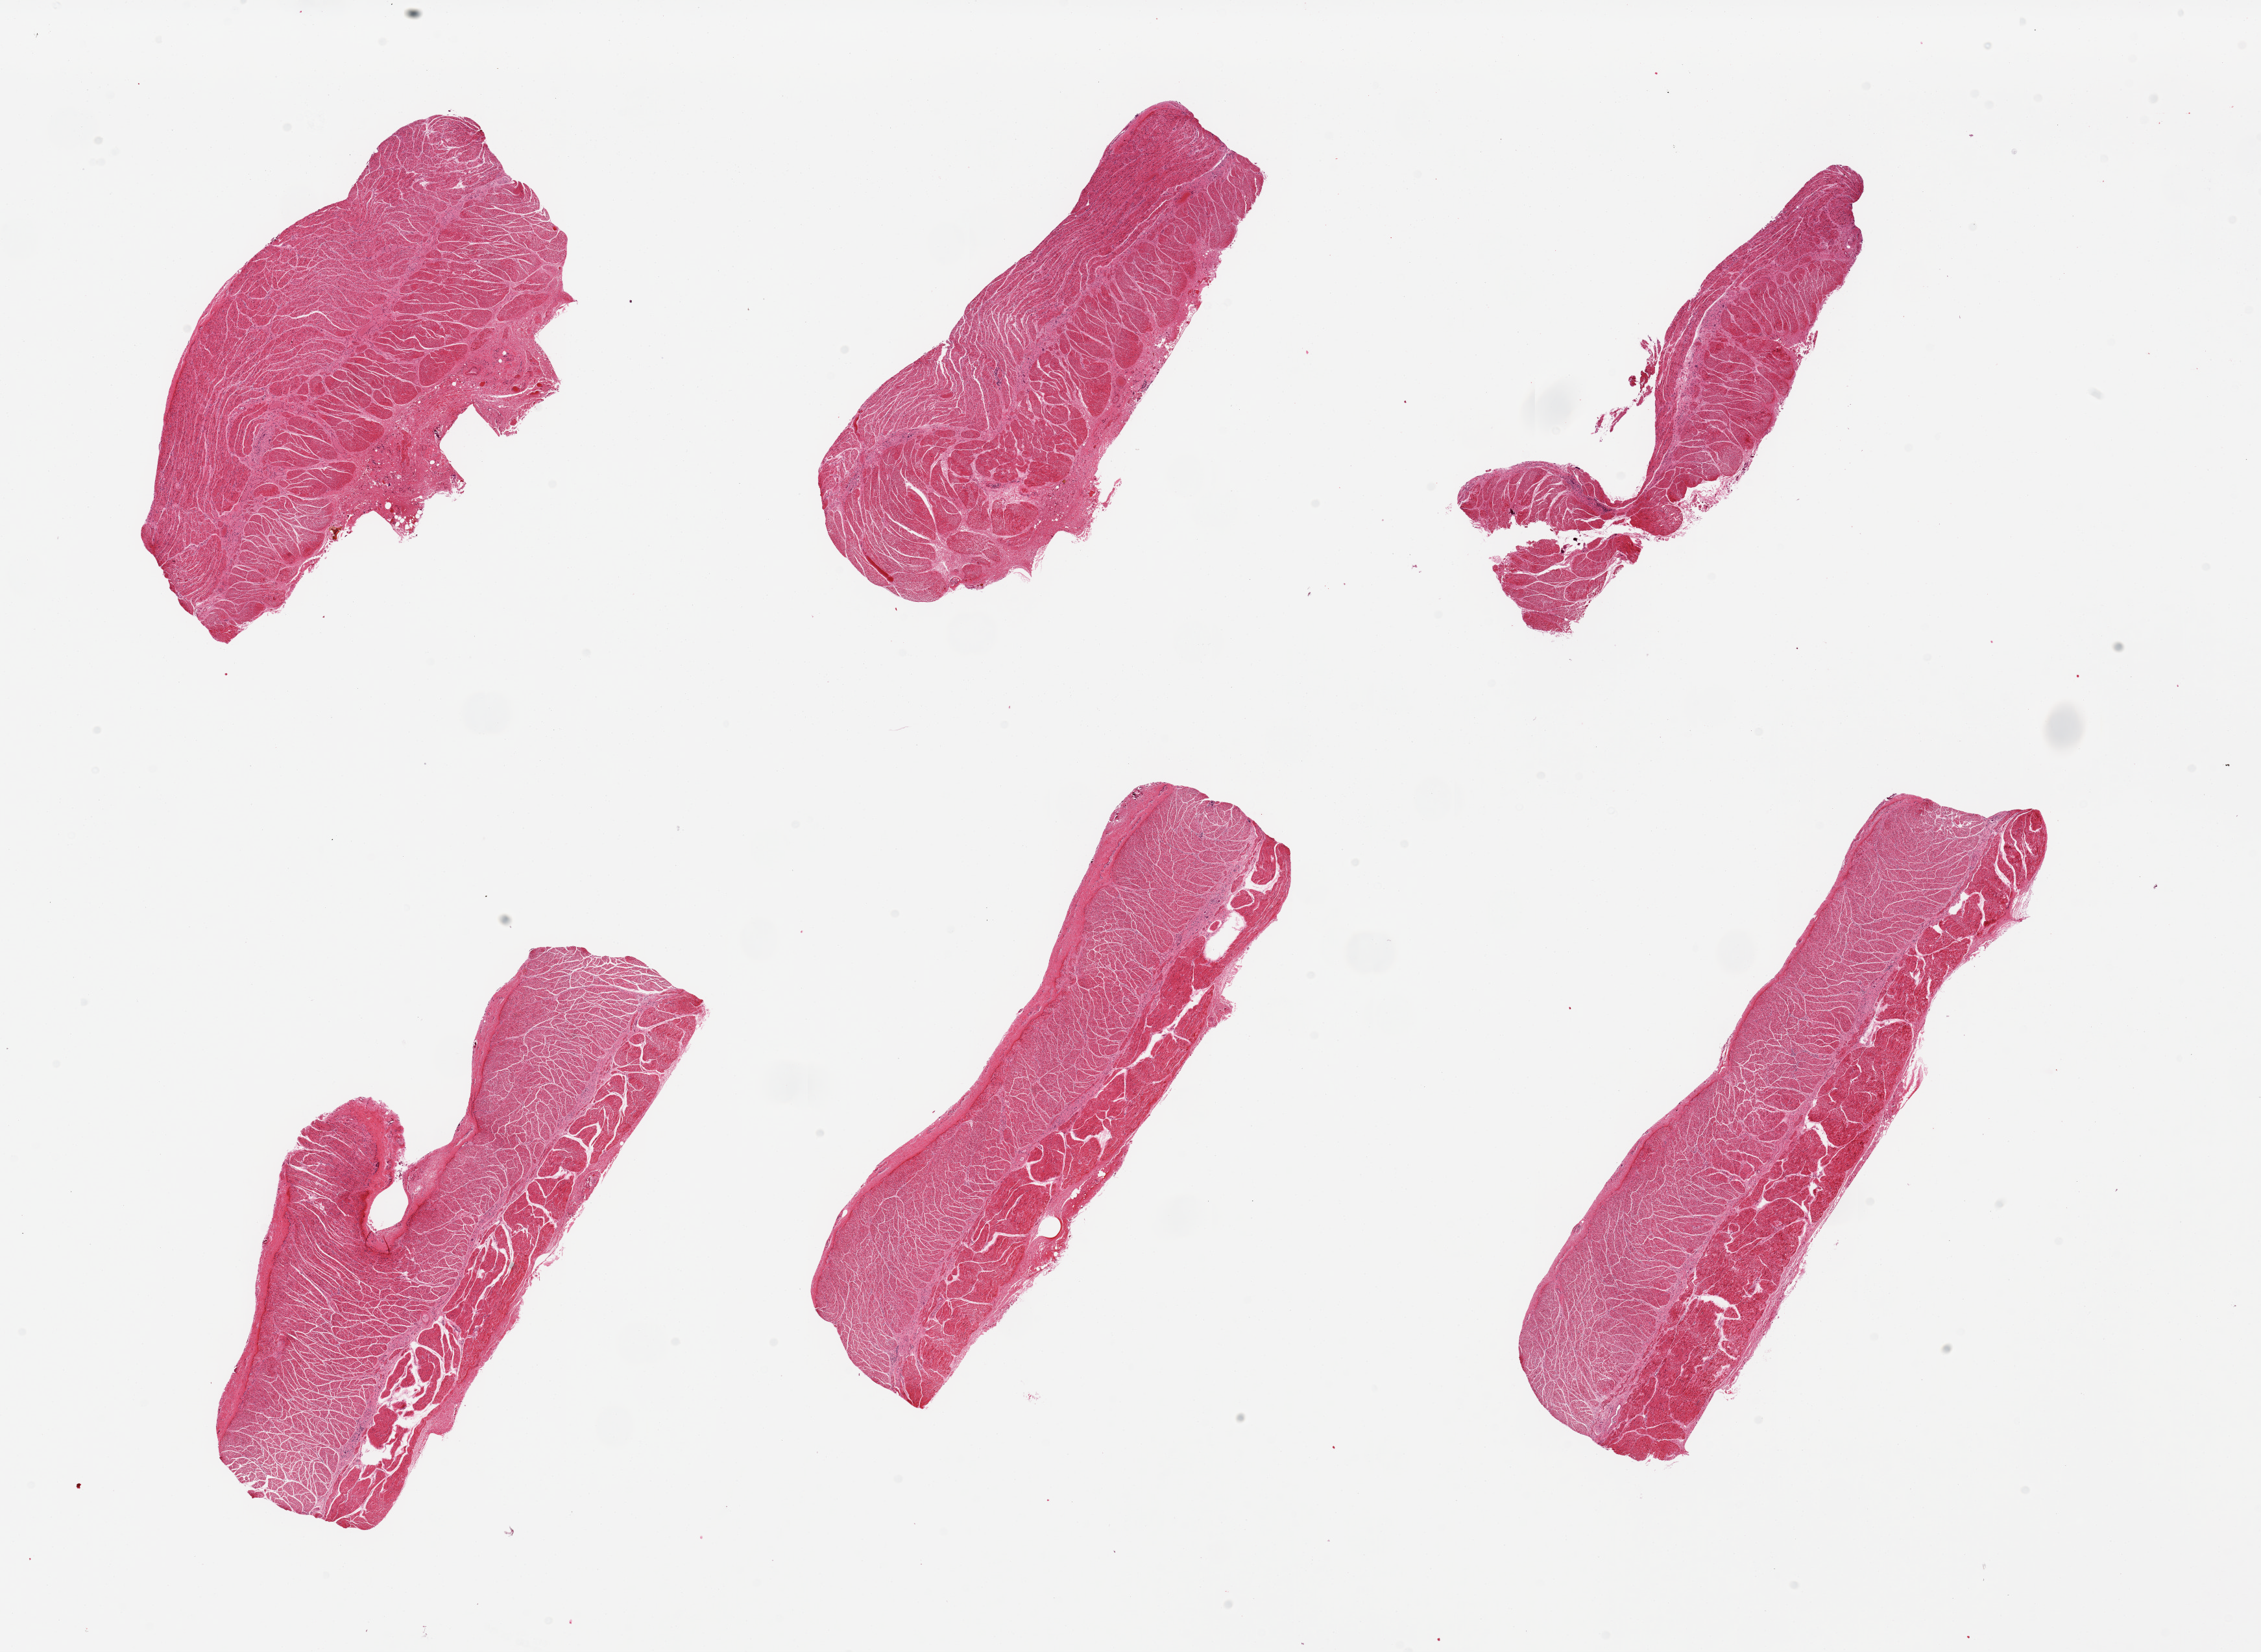
Whole-slide image, haematoxylin and eosin stain, whole scanned area (about 27.6 x 20.1 mm, slide scanned at 20x) shown as a low-resolution overview. PAXgene-fixed, paraffin-embedded tissue. Sampled site (target tissue): esophageal muscle. Donor tissue sample.
Review note (as recorded): 6 pieces, all muscularis, good specimens.